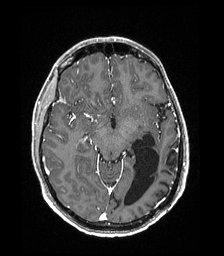
Brain MRI from a brain-tumour surgery series, one axial slice; slice 106 of 192 in the series (ordered by position); T1-weighted post-contrast; 1 mm slice thickness; 224 × 256 image matrix. From the clinical record (not read from this slice): histopathology: Low grade glioma; IDH mutation: no; tumour location: Left Parieto-Occipital Intraventricular.
Outlined on this slice (manually delineated by an expert):
- previous resection cavity: box from (x=124, y=133) to (x=159, y=206) px